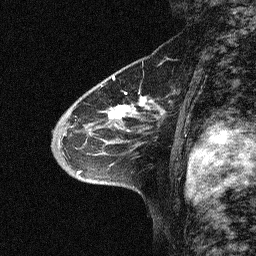
Breast MRI (dynamic contrast-enhanced), one sagittal slice. Position 41 of 64 along the scan axis. Dynamic contrast-enhanced study with each time point stored as its own series, time point 2 of 3 at this slice position (early post-contrast, ordered by acquisition time). 1.5 T. TE 4.5 ms, TR 11 ms. 2.06 mm slice thickness. 256 × 256 image matrix. Female patient, age 46 years. Case-level facts recorded for this patient, not image findings: setting: breast cancer imaged before/during neoadjuvant chemotherapy; receptor status: HER2-positive.
Outlined on this slice (semi-automatically segmented with operator editing):
- analysis volume of interest (the breast-tissue region the enhancement analysis was run in; not a lesion): bounding box <46,51,180,169> (left, top, right, bottom; pixels)
- tumour enhancement mask (voxels above the 90 % enhancement threshold inside the analysis volume of interest): <108,96,158,118>